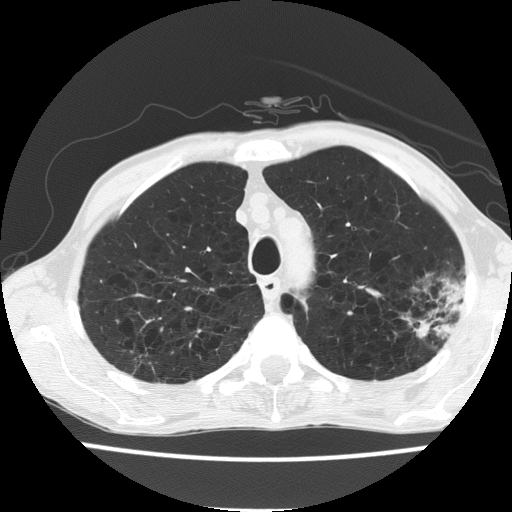
Axial slice from a low-dose chest CT screening exam, first (baseline) screen, lung window (W 1500 / L -600 HU), lung (sharp) reconstruction kernel (FC51), 512 × 512 image matrix. Male, age 60 years at enrolment. Current smoker at enrolment.
Expert-annotated lung lesion, bounding box [x1, y1, x2, y2] px = [393, 268, 467, 344]. No non-calcified nodule or mass ≥4 mm was recorded by the screening reader at this exam. Official screen result: negative screen, minor abnormalities not suspicious for lung cancer.